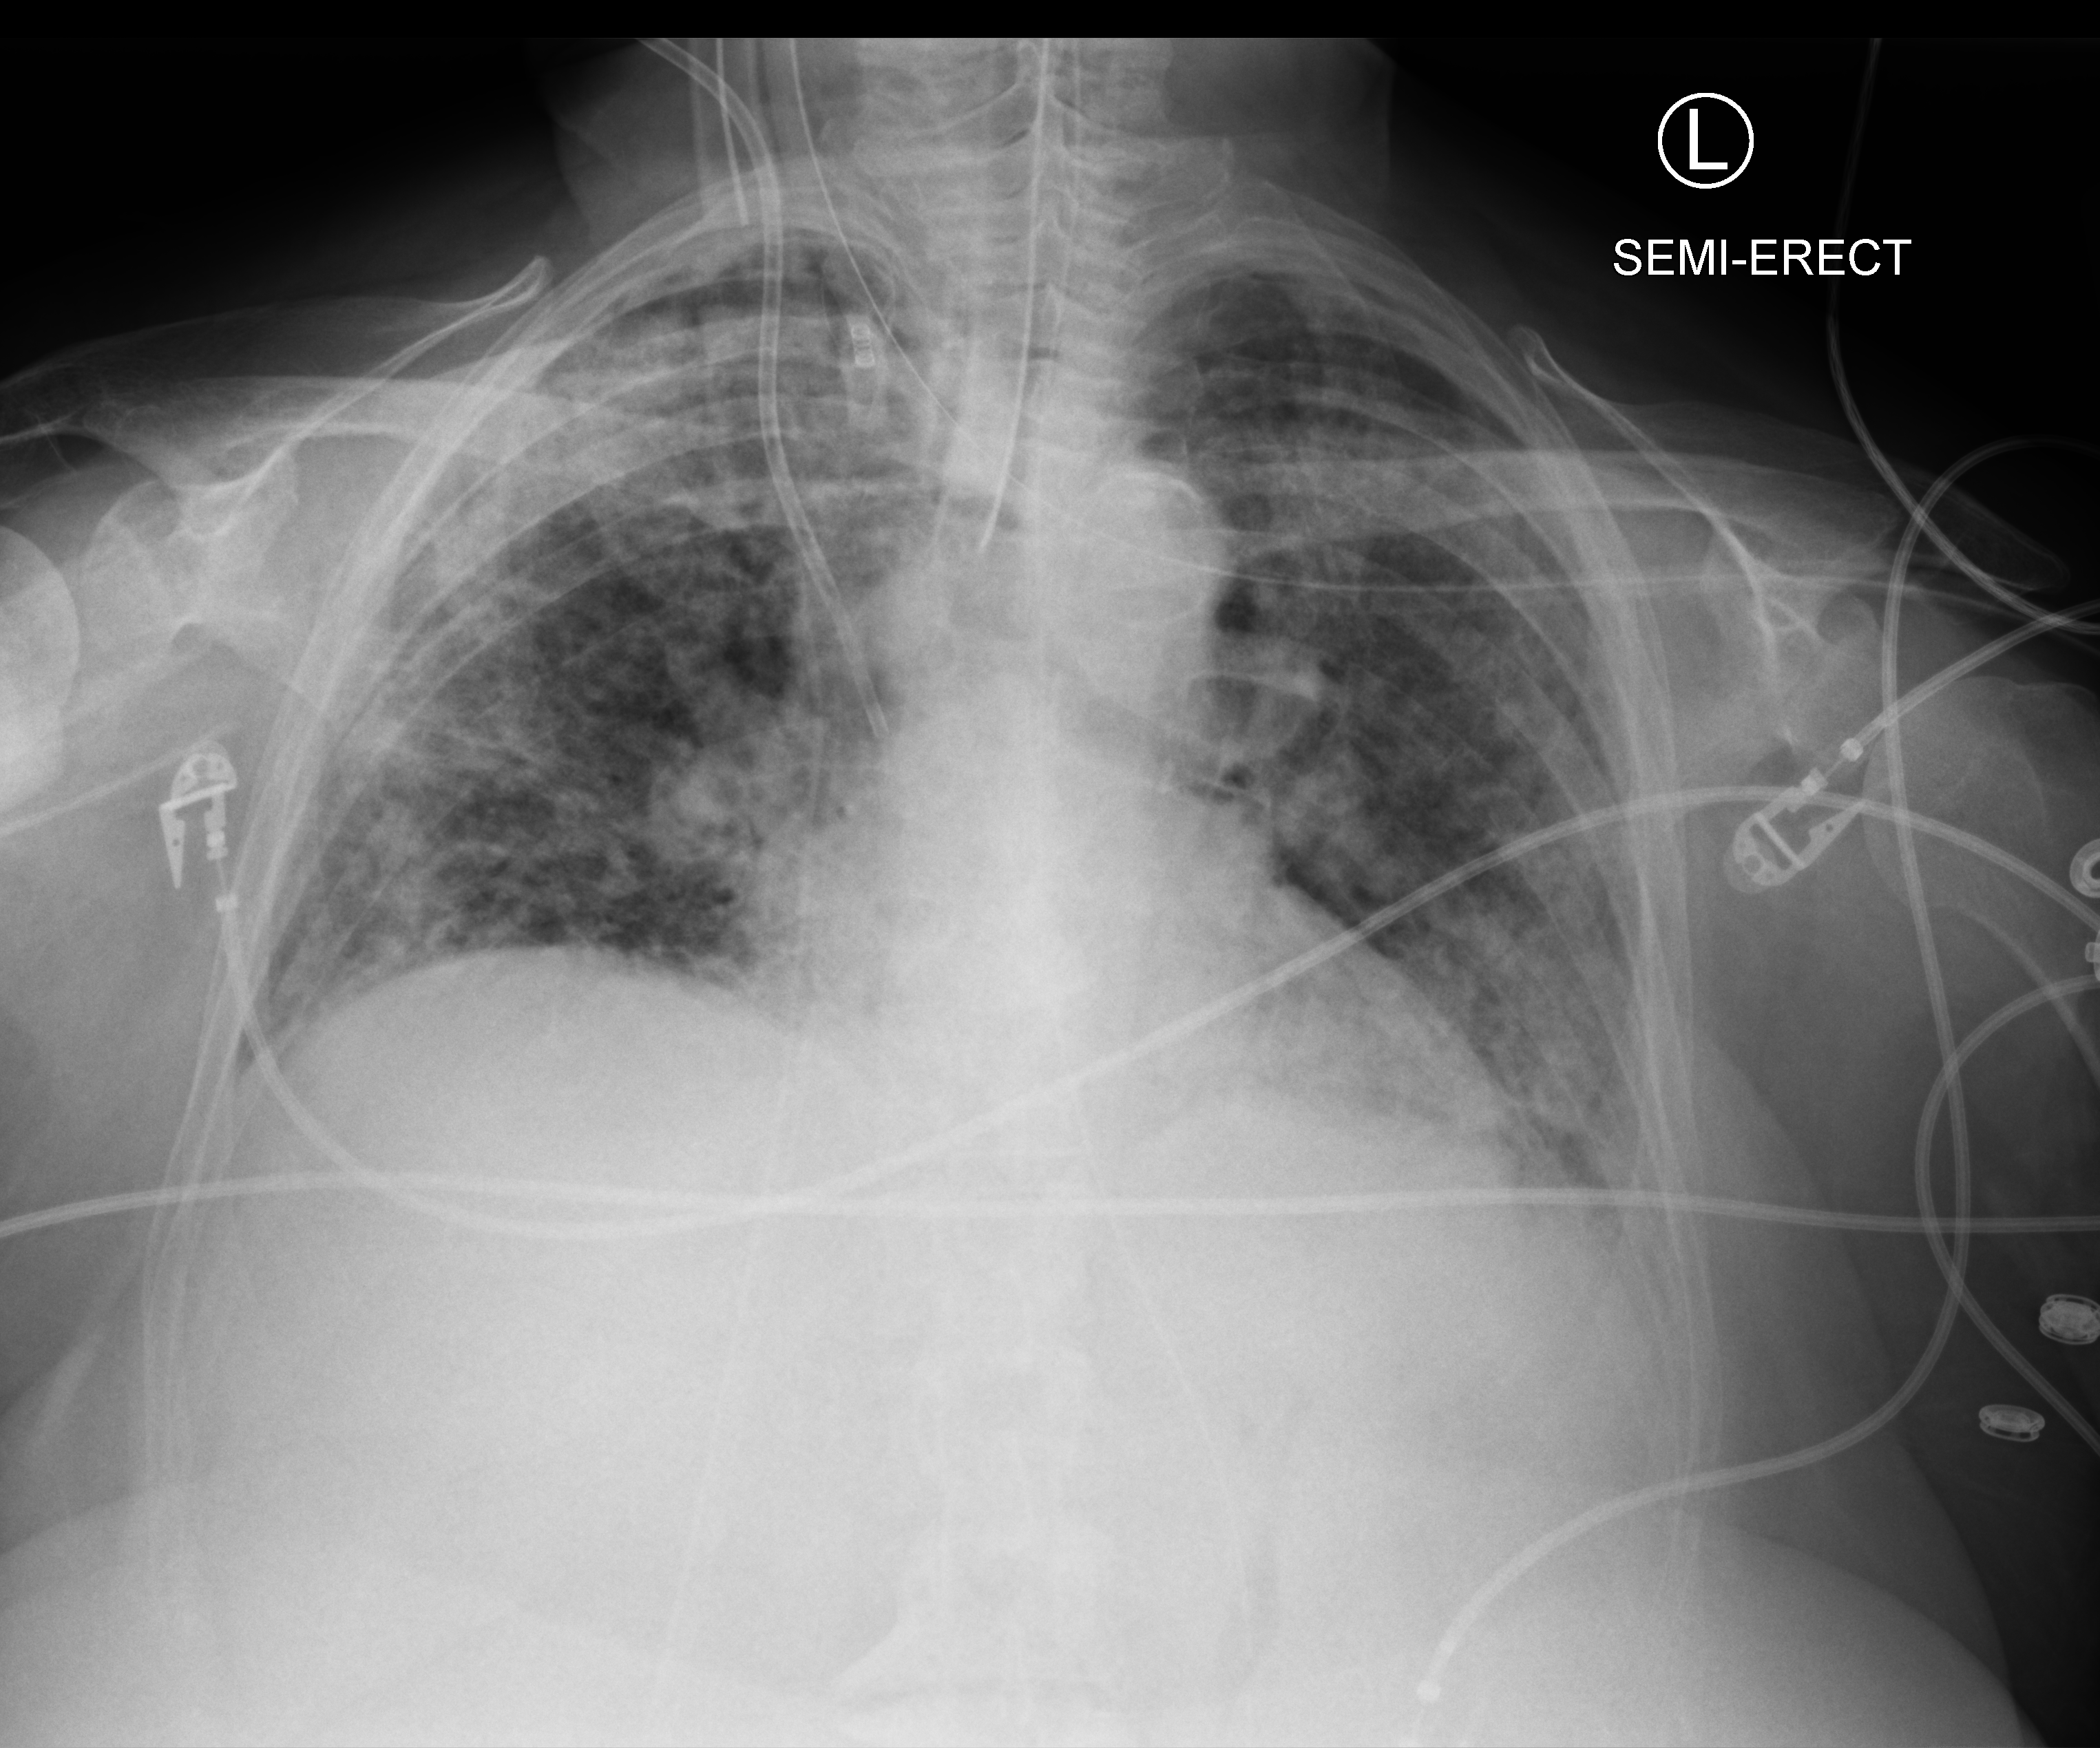
Bedside chest radiograph (computed radiography); anteroposterior (AP) projection. Female patient hospitalised with COVID-19, age 75–90 years.
Admission-level facts for this patient (not findings on this image; timing relative to this image not recorded):
- other chronic lung disease (admission record): no